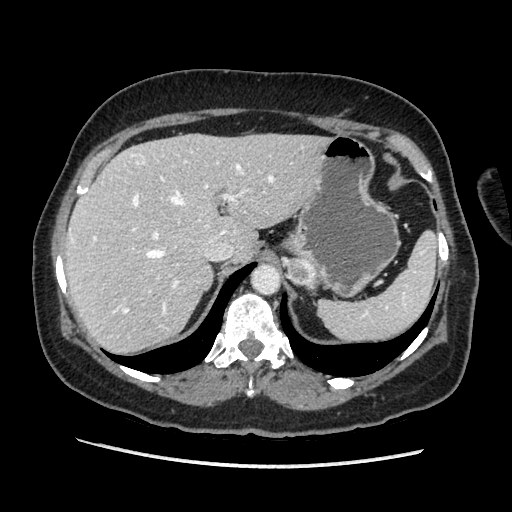
Contrast-enhanced abdominal CT, one axial slice. Slice 146 of 203 in the series (ordered by position). Soft-tissue window (W 400 / L 40 HU). 512 × 512 image matrix. Female patient. Case-level facts recorded for this patient, not image findings: diagnosis: adrenocortical carcinoma; tumour side: left adrenal; tumour size at pathology: 6.5 cm; Ki-67 index: 22 %; stage (as recorded): 2.
Outlined on this slice (semi-automatically segmented with operator editing):
- mass: bounding box <287,259,315,284> (left, top, right, bottom; pixels)